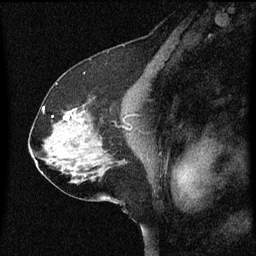
Breast MRI (dynamic contrast-enhanced), one sagittal slice. Position 37 of 60 along the scan axis. Dynamic contrast-enhanced series, image 2 of 3 at this slice position (ordered by acquisition). 1.5 T. TE 4.2 ms, TR 8 ms. 2 mm slice thickness. 256 × 256 image matrix. Female patient, age 58 years.
Structures marked on this image (semi-automatic segmentation, software-assisted and operator-edited):
- analysis volume of interest (the breast-tissue region the enhancement analysis was run in; not a lesion): bounding box [x1, y1, x2, y2] px = [56, 104, 95, 137]
- tumour enhancement mask (voxels above the 70 % enhancement threshold inside the analysis volume of interest): [64, 112, 79, 123]